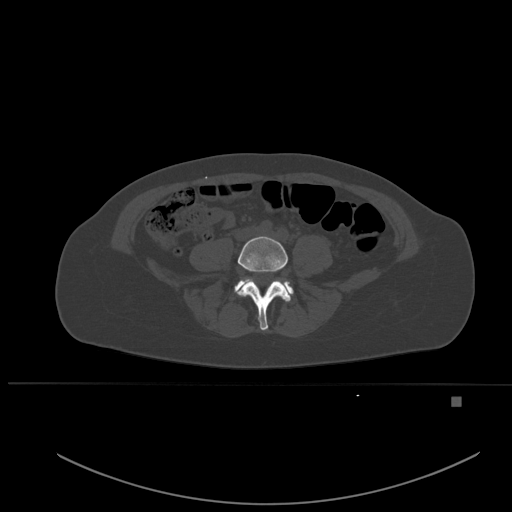
CT including the spine, one axial slice. Position 168 of 651 along the scan axis. Bone window (W 1800 / L 400 HU). 1.5 mm slice thickness. 512 × 512 image matrix. Patient: female, 49 years. Case-level facts recorded for this patient, not image findings: primary cancer: breast; vertebrae with lytic lesions (as recorded): L3, T12, L4.
Structures marked on this image (semi-automatic segmentation, software-assisted and operator-edited):
- L4 vertebra: box from (x=238, y=236) to (x=291, y=330) px
- L5 vertebra: (x=234, y=278)–(x=294, y=297)